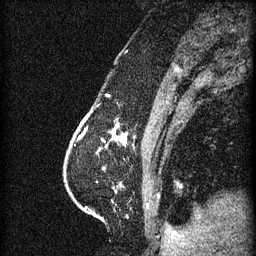
Breast MRI (dynamic contrast-enhanced), one sagittal slice; slice 19 of 60 in the series (ordered by position); 3 images stored at this slice position (order not interpretable as contrast timing); 1.5 T; TE 4.2 ms, TR 11 ms; 1.5 mm slice thickness; 256 × 256 image matrix, field of view 180 × 180 mm. Patient: female, 63 years.
Annotated regions visible in this slice (semi-automatic segmentation, software-assisted and operator-edited):
- analysis volume of interest (the breast-tissue region the enhancement analysis was run in; not a lesion): bounding box [x1, y1, x2, y2] px = [86, 118, 129, 153]
- tumour enhancement mask (voxels above the 70 % enhancement threshold inside the analysis volume of interest): [104, 128, 127, 143]